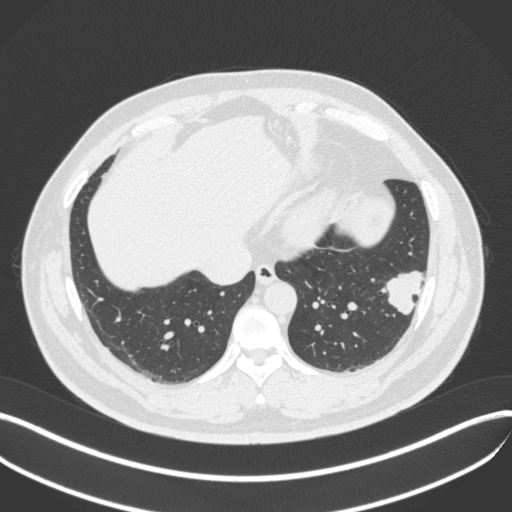
Chest CT, one axial slice. Reconstruction kernel B31f. Lung window (W 1500 / L -600 HU). 1 mm slice thickness. 512 × 512 image matrix, field of view 400 × 400 mm. Male patient, age 39 years. From the clinical record (not read from this slice): clinical TNM (as recorded): T2a N0 M0.
Annotated regions visible in this slice (bounding box drawn by a radiologist):
- lung tumour (recorded histology: adenocarcinoma): bounding box <379,265,433,318> (left, top, right, bottom; pixels)